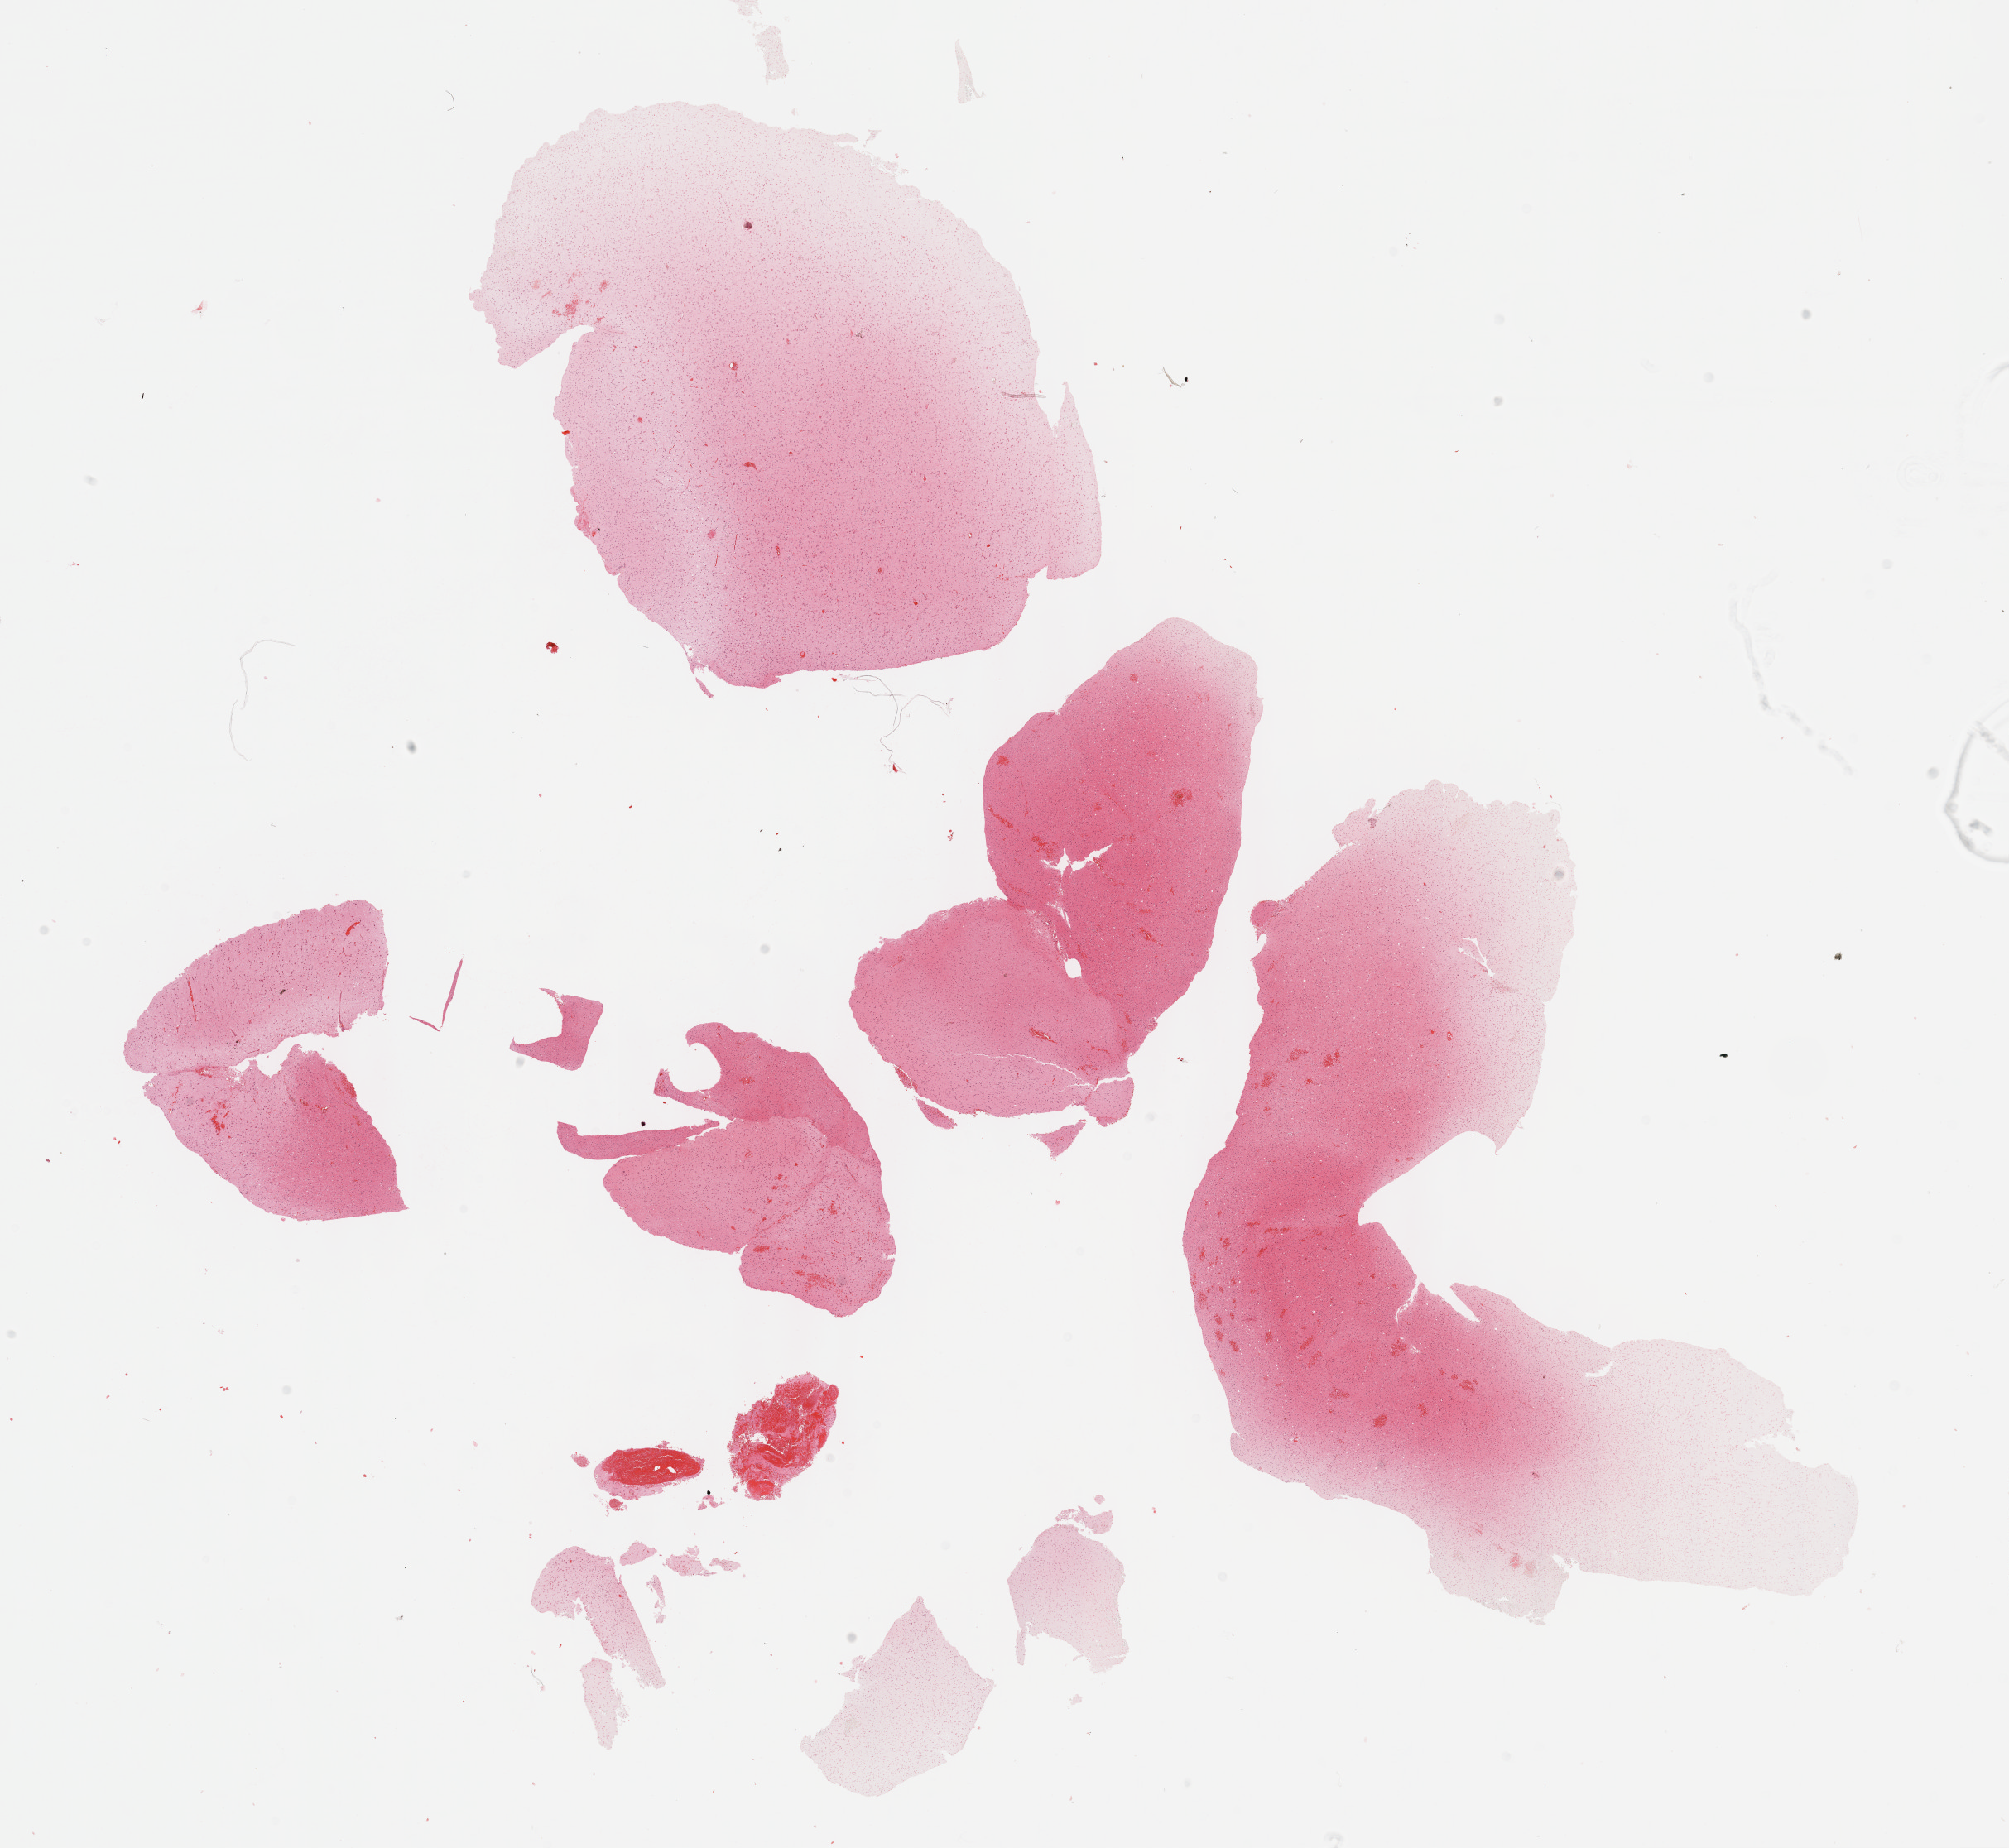
Whole-slide histology image, H&E, shown as a low-resolution overview of the whole scanned area (about 19.6 x 18.1 mm, from a 40x scan); formalin-fixed paraffin-embedded (FFPE) diagnostic section; brain, primary tumour sample. Patient: male, age at initial diagnosis 33 years.
Diagnosis: Astrocytoma, NOS (cerebrum).